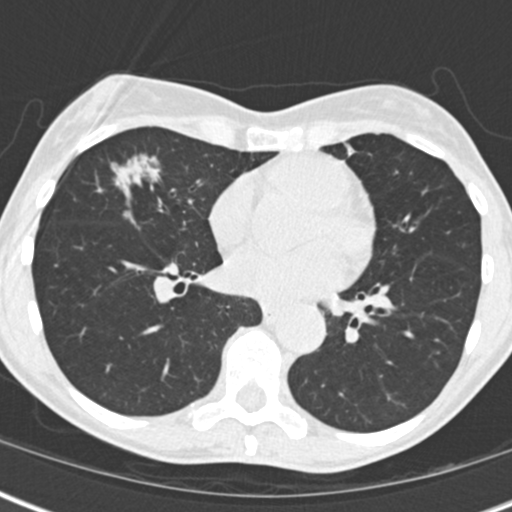
Low-dose screening chest CT, one axial slice. Position 75 of 173 along the scan axis. Reconstruction kernel B30f. 120 kVp. Lung window (W 1500 / L -600 HU). 2 mm slice thickness. 512 × 512 image matrix, field of view 290 × 290 mm.
Annotated regions visible in this slice (outlined manually by an expert reader):
- lesion 1 (tumor, middle lobe of right lung): bounding box [x1, y1, x2, y2] px = [115, 157, 159, 191]